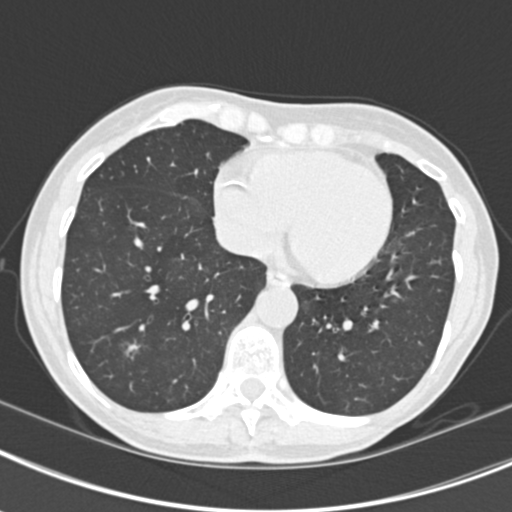
Axial slice from a low-dose chest CT screening exam; second screening round (one year after baseline); lung window (W 1500 / L -600 HU); 2 mm slice thickness; standard (soft-tissue) reconstruction kernel (B30f); slice 134 of 219 in the series; 512 × 512 image matrix, field of view 298 × 298 mm. Female participant, aged 63 years at enrolment. Current smoker at enrolment.
Lesion marked by an expert reader, bounding box <110,327,153,370> (left, top, right, bottom; pixels). The screening reader recorded 9 non-calcified nodules or masses ≥4 mm on this exam (left upper lobe, right upper lobe, left upper lobe, left lower lobe, right middle lobe, left lower lobe, left lower lobe, right lower lobe, right lower lobe); which of them this box marks is not recorded. Lung cancer was diagnosed 408 days after this screen: bronchiolo-alveolar adenocarcinoma, NOS, right upper lobe, right middle lobe, right lower lobe, left upper lobe, left lower lobe, moderately differentiated (G2), stage IV (AJCC 6th edition).